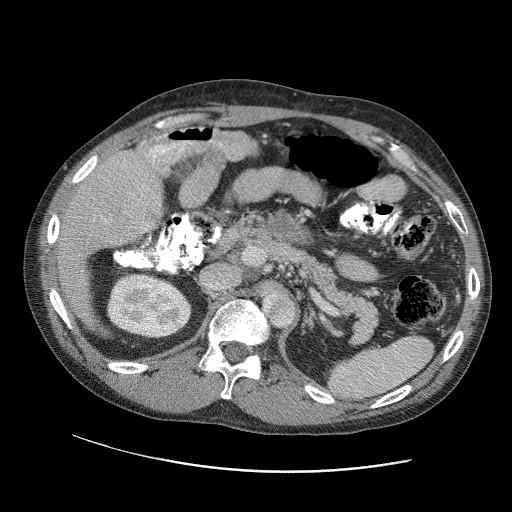
Contrast-enhanced abdominal CT (liver protocol), one axial slice; slice 58 of 109 in the series (ordered by position); soft-tissue window (W 400 / L 40 HU); 2.5 mm slice thickness; 512 × 512 image matrix, field of view 400 × 400 mm. From the clinical record (not read from this slice): diagnosis: hepatocellular carcinoma (patient treated with transarterial chemoembolisation; whether this scan precedes or follows treatment is not stated here); TNM stage (as recorded): Stage-IIIC; Child-Pugh class: B; tumour differentiation: well differentiated; tumour nodularity: uninodular.
Annotated regions visible in this slice (semi-automatic segmentation, software-assisted and operator-edited):
- liver parenchyma outside the tumour (the mass and vessels are separate outlines, so this box may not span the whole liver): bounding box [x1, y1, x2, y2] px = [56, 134, 256, 302]
- liver vessels: [69, 135, 247, 256]